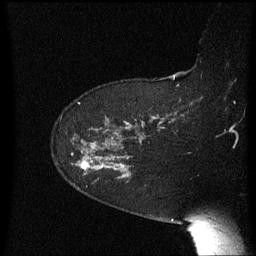
Breast MRI (dynamic contrast-enhanced), one sagittal slice; slice 45 of 60 in the series (ordered by position); dynamic contrast-enhanced series, image 2 of 3 at this slice position (ordered by acquisition); 1.5 T; TE 4.2 ms, TR 8.4 ms; 2.3 mm slice thickness; 256 × 256 image matrix, field of view 200 × 200 mm. Patient: female, 63 years. Case-level facts recorded for this patient, not image findings: setting: breast cancer imaged before/during neoadjuvant chemotherapy; receptor status: HER2-positive.
Annotated regions visible in this slice (semi-automatic segmentation, software-assisted and operator-edited):
- analysis volume of interest (the breast-tissue region the enhancement analysis was run in; not a lesion): bounding box [x1, y1, x2, y2] px = [72, 136, 138, 187]
- tumour enhancement mask (voxels above the 70 % enhancement threshold inside the analysis volume of interest): [81, 162, 88, 169]